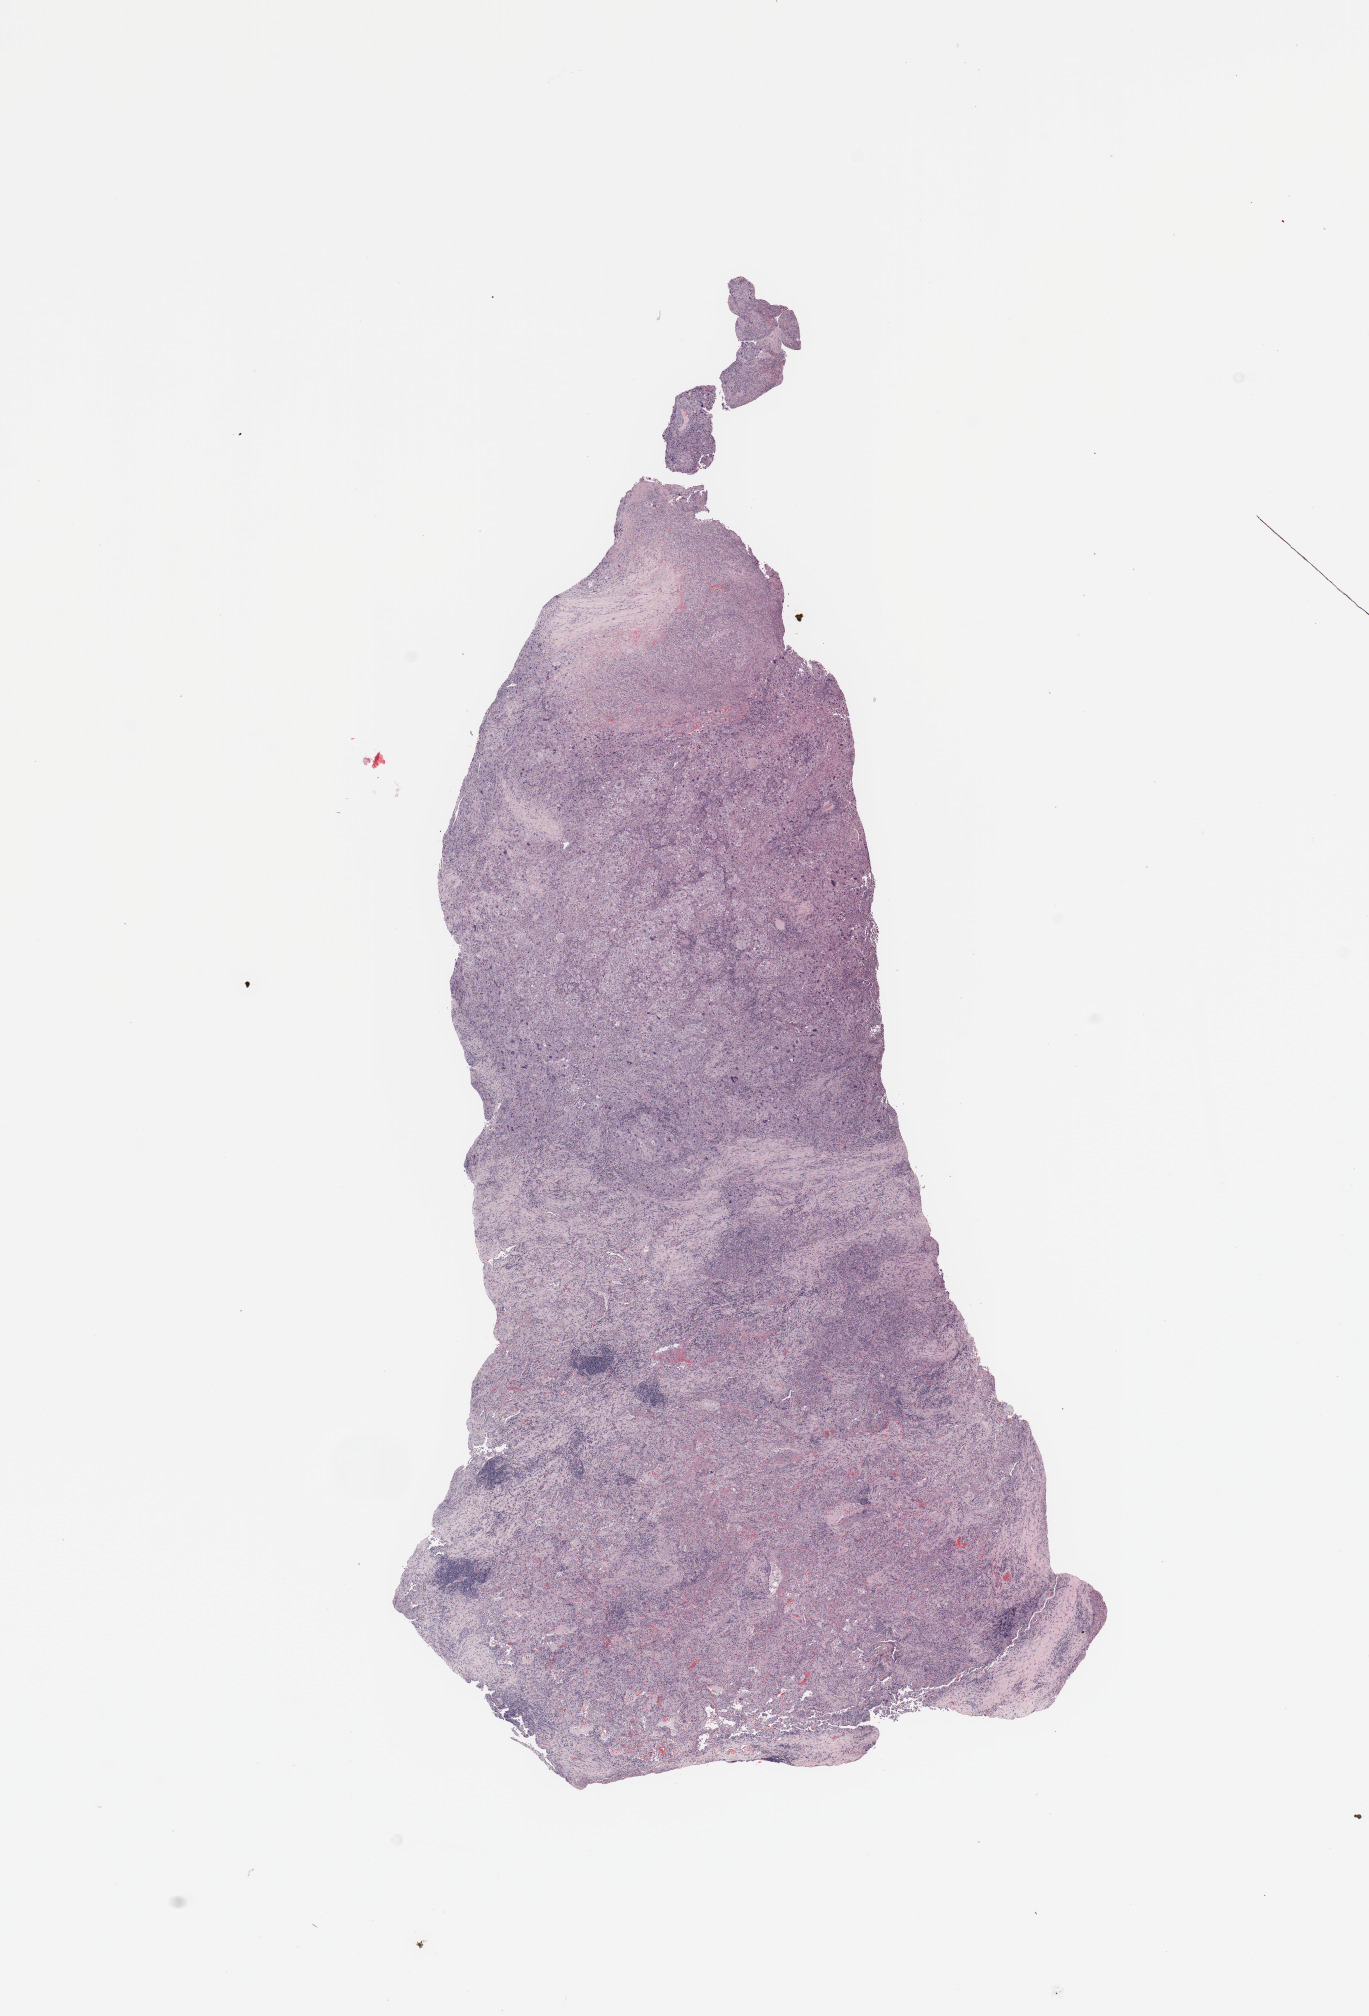
Digitized H&E-stained tissue section (whole slide), a low-resolution overview of the entire scanned area, about 10.8 x 15.9 mm (slide scanned at 20x); lung, tumour tissue. Female, 66 y/o. Histologic grade: G3 (poorly differentiated).
* diagnosis: Adenocarcinoma, NOS
* AJCC pathologic stage: IIA